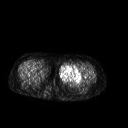
FDG PET of an extremity soft-tissue mass (from a PET/CT study), one axial slice. Slice 240 of 267 in the series (ordered by position). 3.27 mm slice thickness. 128 × 128 image matrix, field of view 500 × 500 mm. Female patient, age 42 years. From the clinical record (not read from this slice): histological type: pleiomorphic leiomyosarcoma; grade: intermediate; site of the primary tumour: left thigh.
Annotated regions visible in this slice (expert contour drawn on MRI and transferred to this co-registered scan by the dataset authors):
- gross tumour volume including surrounding oedema: bounding box (x1, y1, x2, y2) in pixels: (59, 64, 82, 83)
- gross tumour volume (mass): (59, 64, 82, 83)